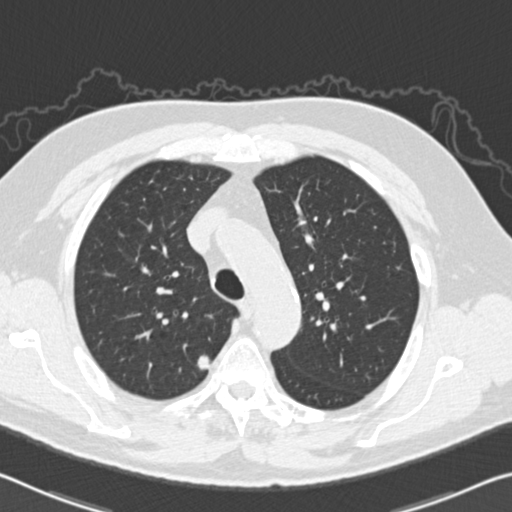
Chest CT (low-dose screening protocol), one axial image. Baseline screening round. Lung window (W 1500 / L -600 HU). 2 mm slice thickness. Standard (soft-tissue) reconstruction kernel (B30f). Male, age 64 years at enrolment.
Expert-annotated lung lesion, box from (x=185, y=342) to (x=229, y=385) px. Reader record for this screening exam (exam-level; its link to the box is not recorded): non-calcified nodule or mass ≥4 mm, right upper lobe, 10 × 8 mm, spiculated (stellate) margins, soft tissue attenuation. Official screen result: positive, change unspecified: nodule(s) >= 4 mm or enlarging nodule(s), mass(es), or other non-specific abnormalities suspicious for lung cancer. Later outcome: lung cancer diagnosed 99 days after this screen — adenocarcinoma, NOS, right upper lobe, poorly differentiated (G3), stage IA (AJCC 6th edition), 11 mm at pathology.